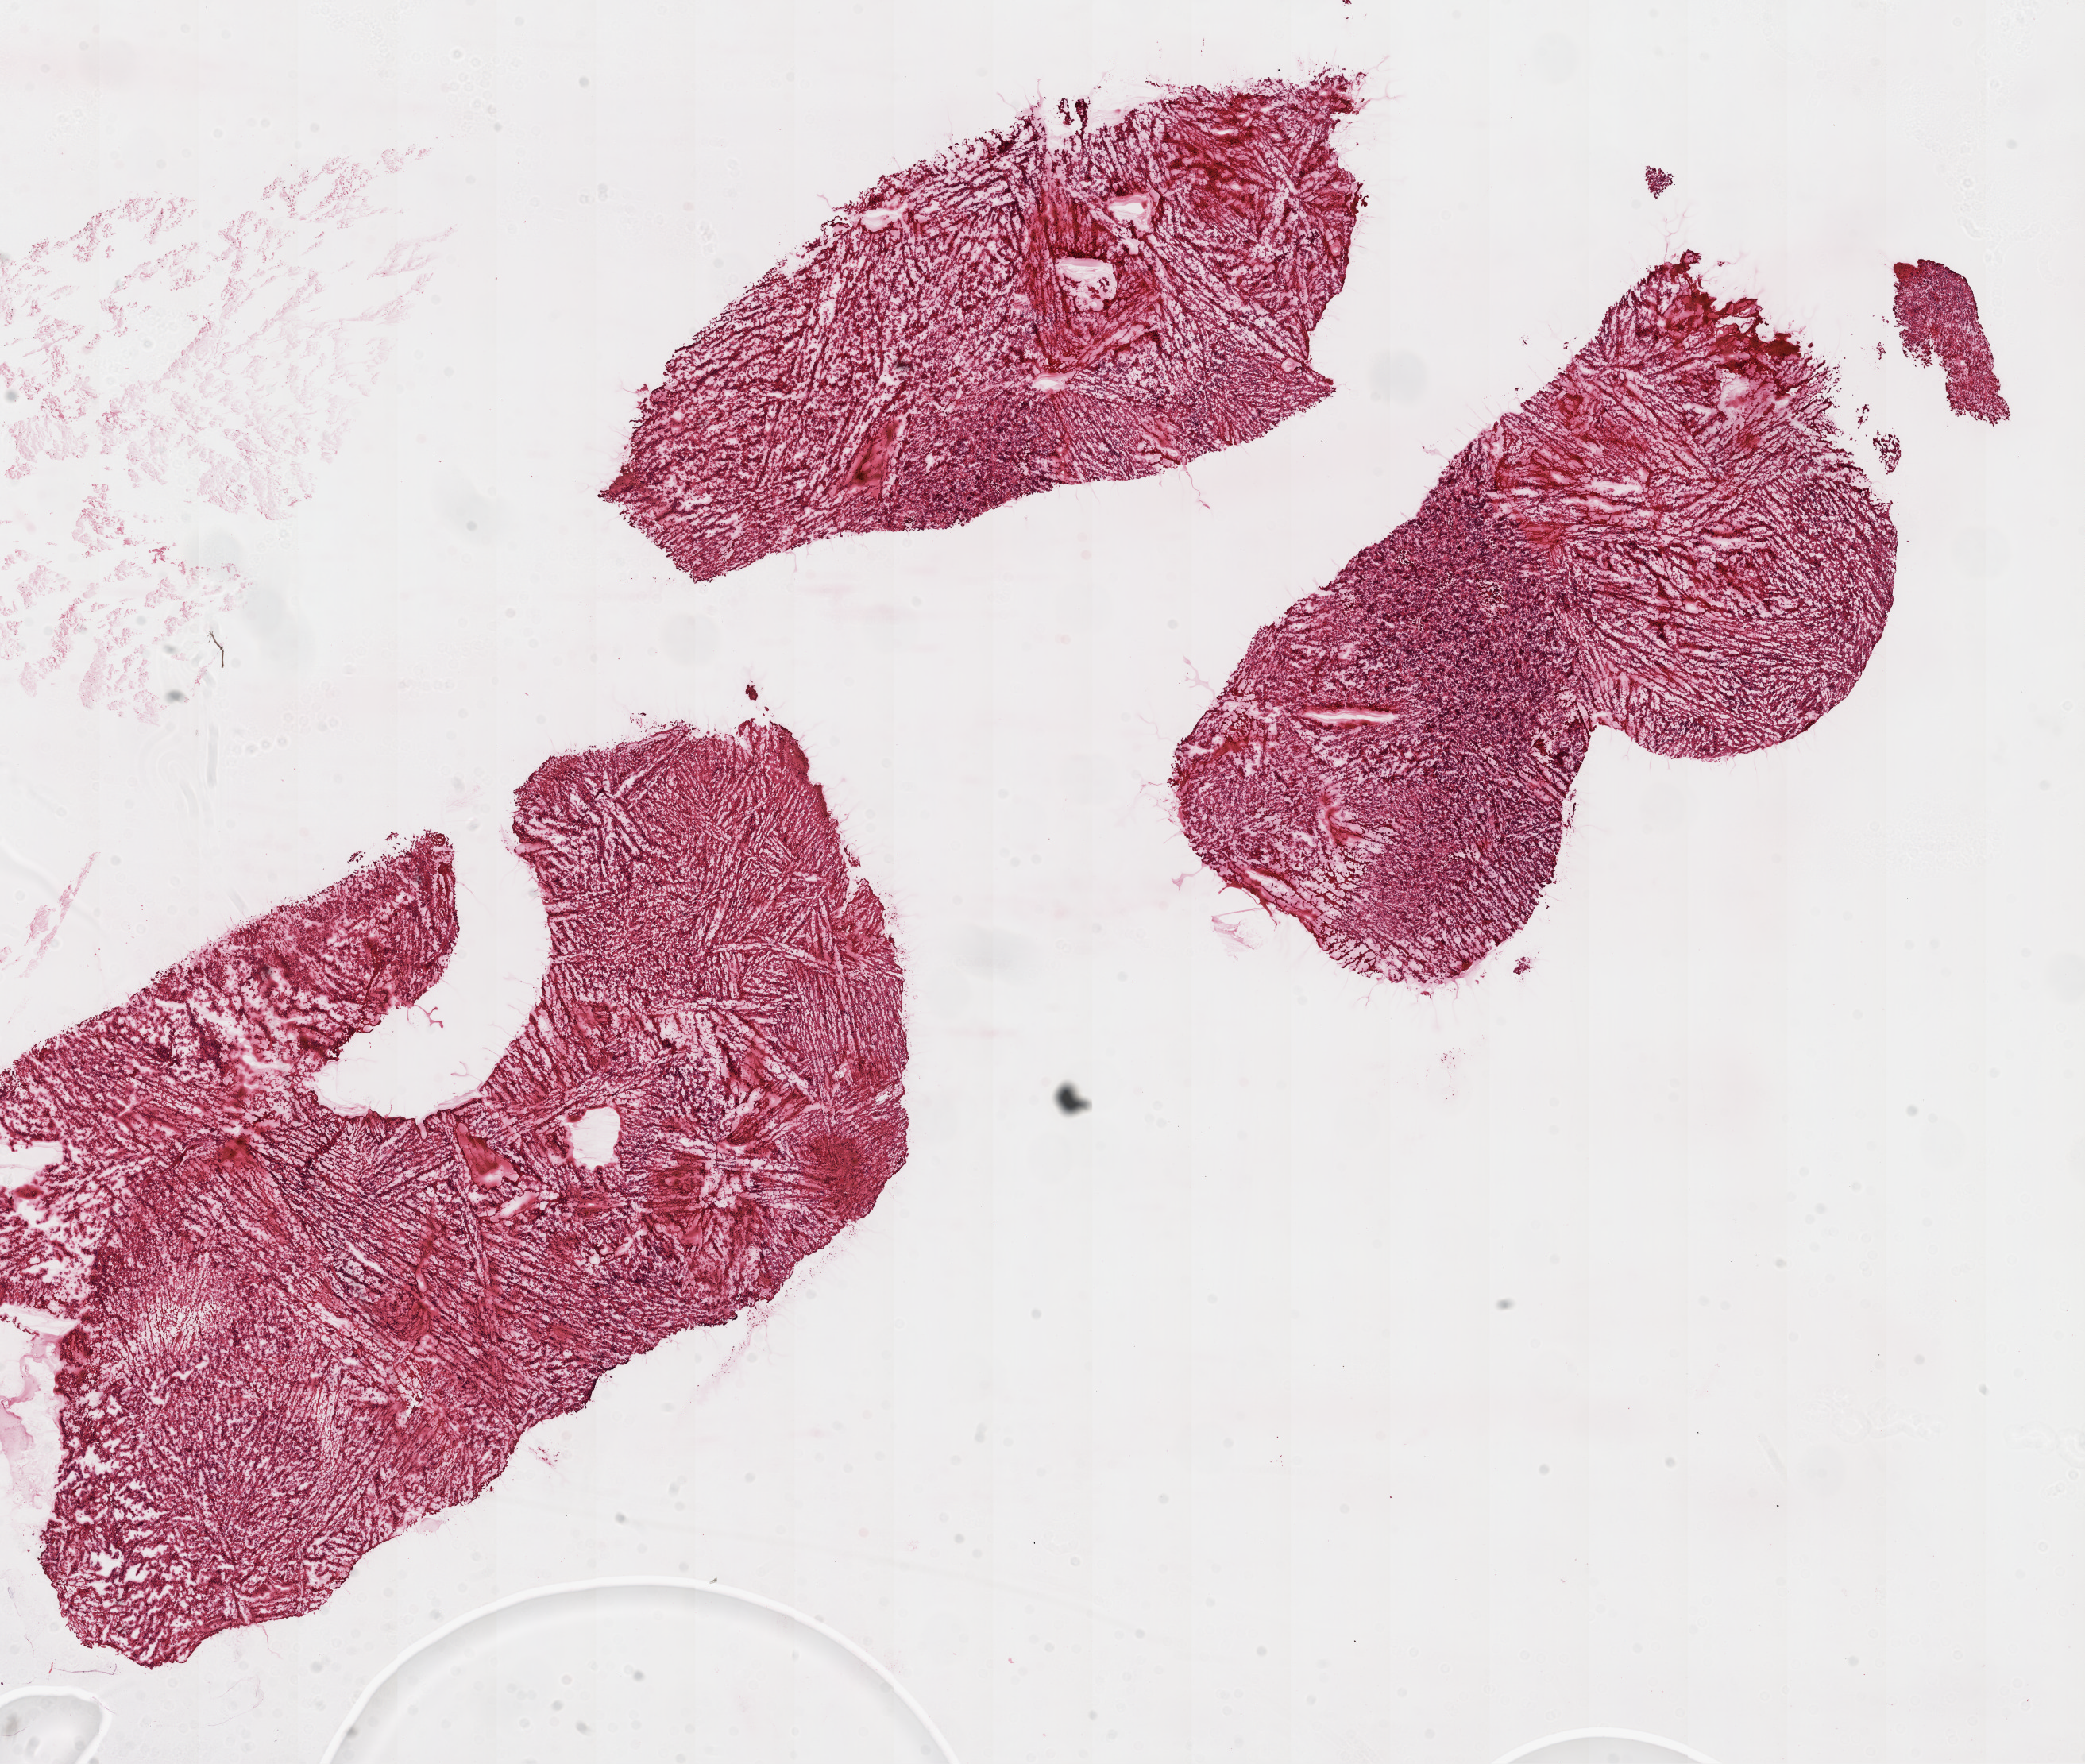
Hematoxylin and eosin (H&E) stained whole-slide image, a low-resolution overview of the entire scanned area, about 21.1 x 17.8 mm. Frozen section from the top of the tissue portion. Primary tumour sample from the brain. Female patient; age at initial diagnosis 76 years. Pathologist review of this section (percent, as recorded): tumour cells 75%, tumour nuclei 80%, normal cells 0%, stromal cells 0%, necrosis 15%.
Pathologic diagnosis: Glioblastoma.